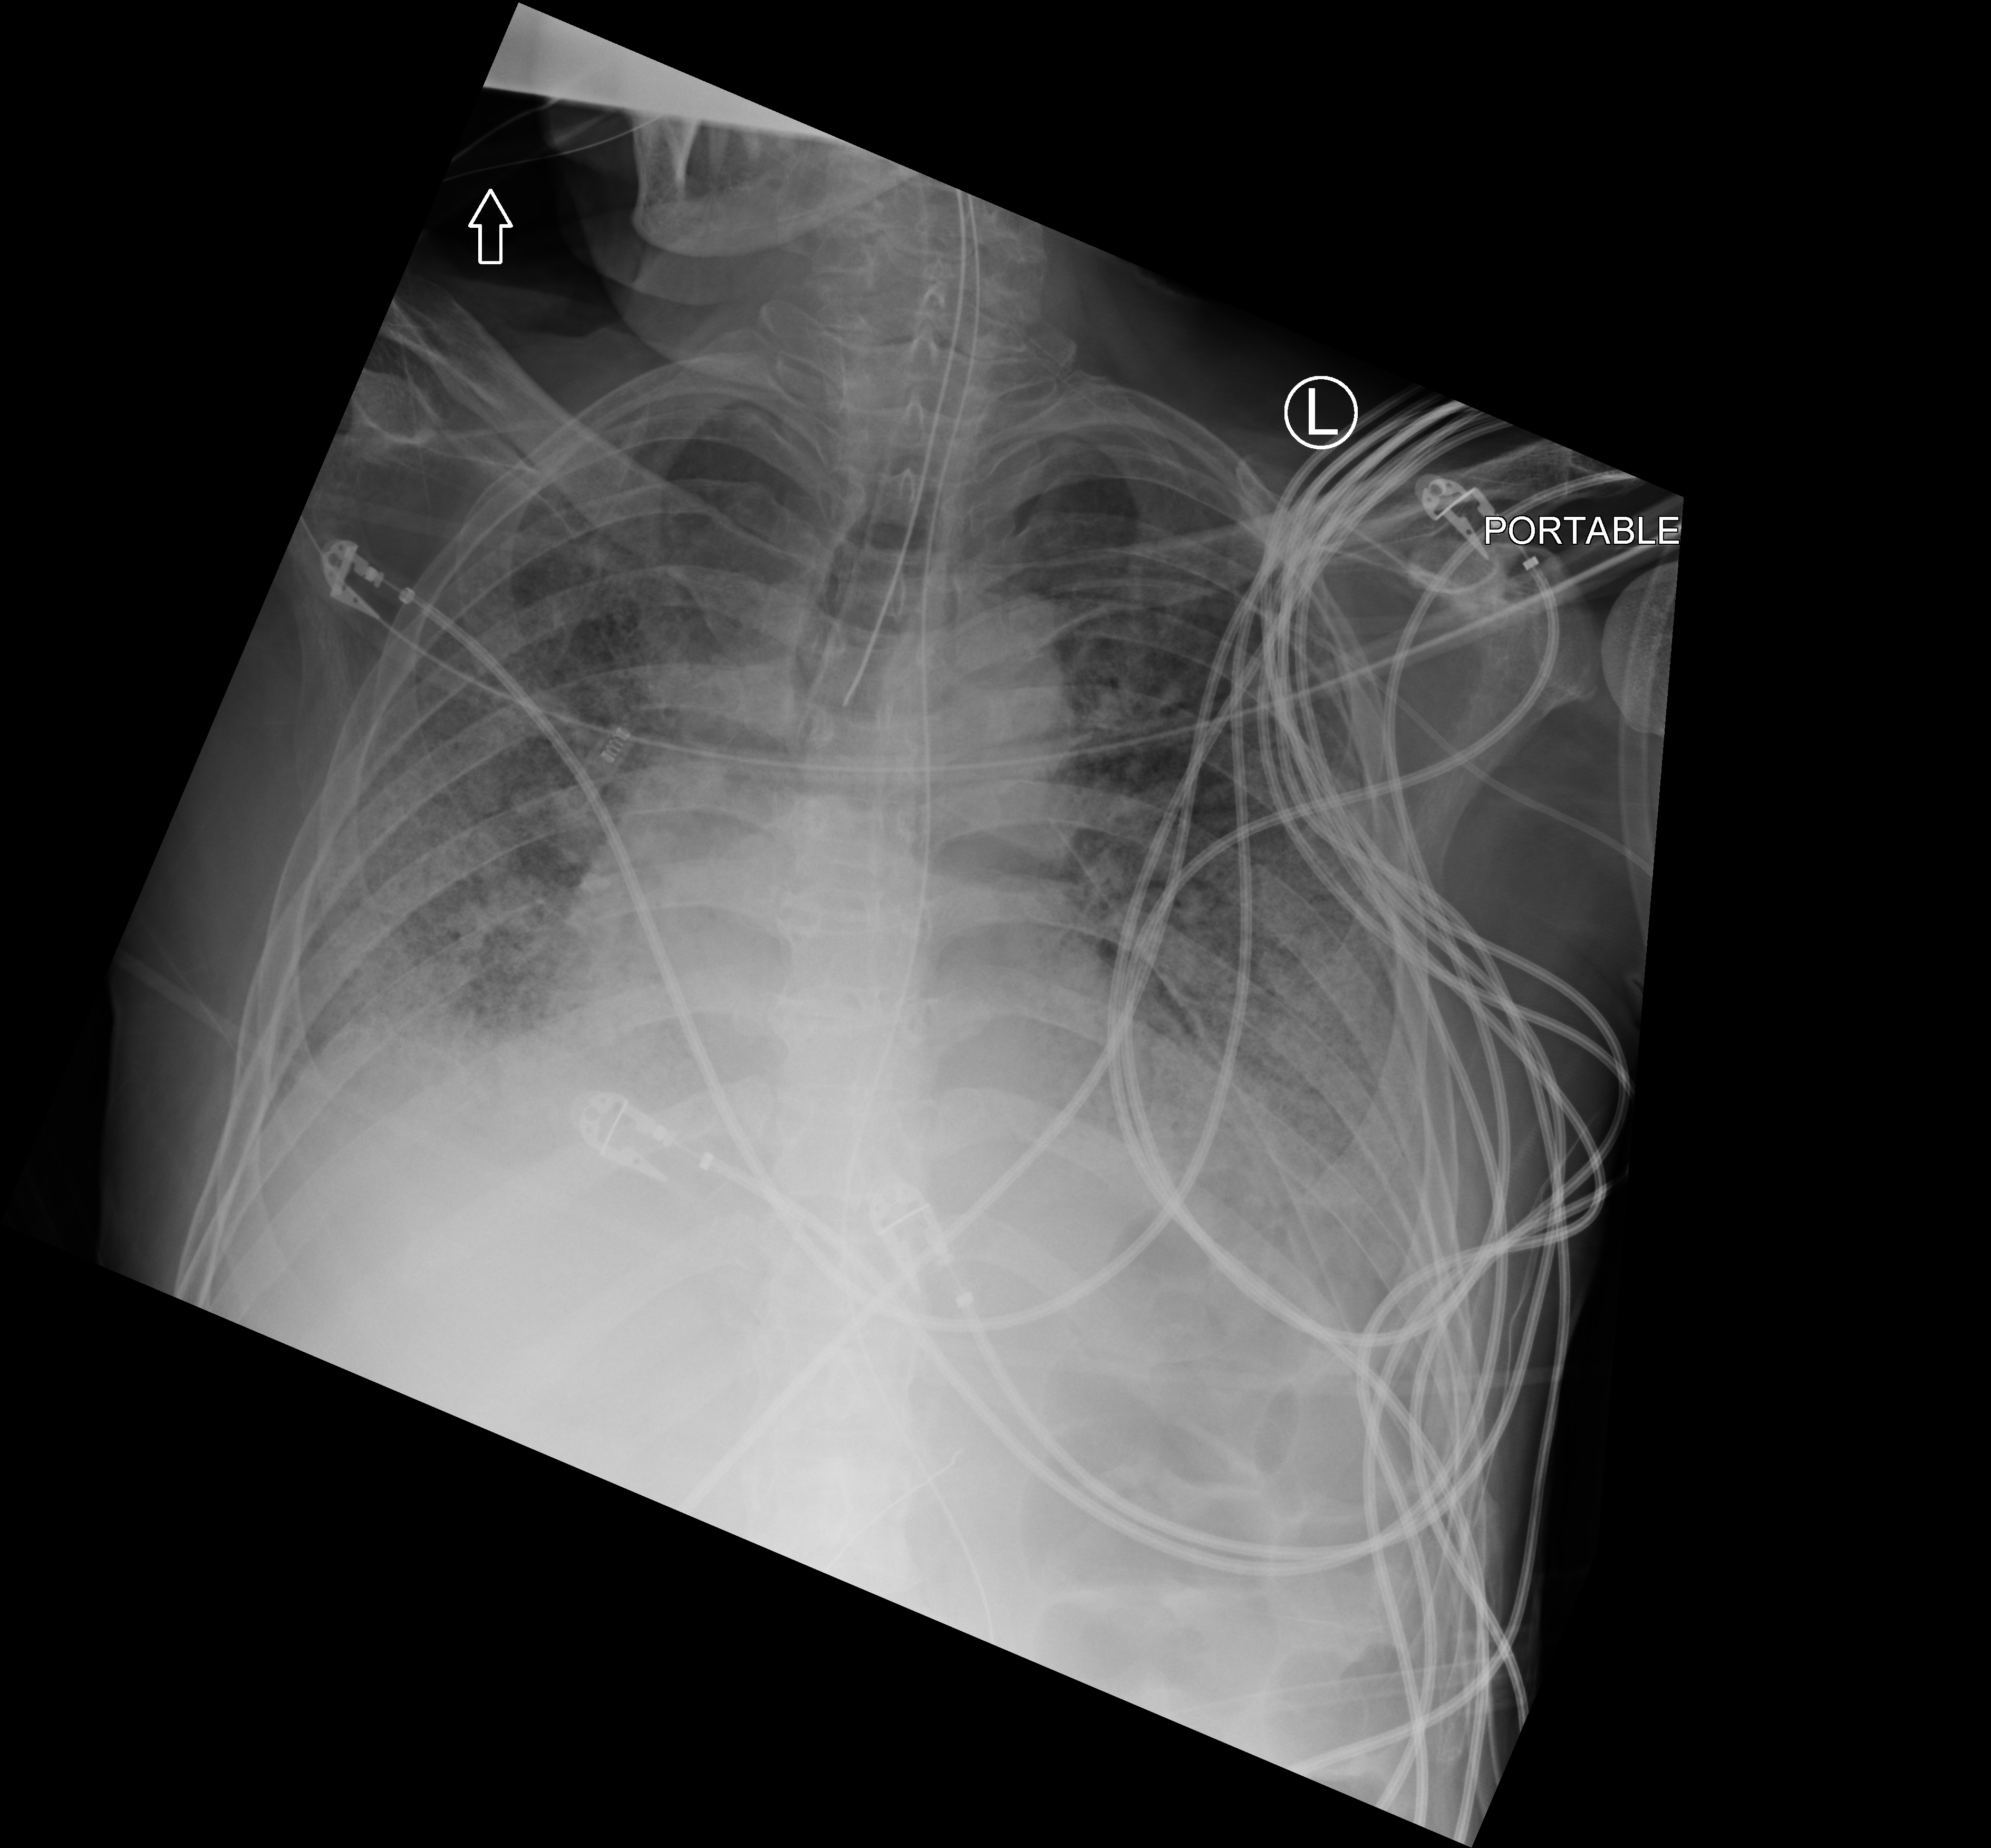
Chest X-ray (portable). Male patient hospitalised with COVID-19, age 60–74 years.
Hospital-stay facts (about this admission, not read from this image; timing relative to this image not recorded): admitted to intensive care during this hospital stay: yes.